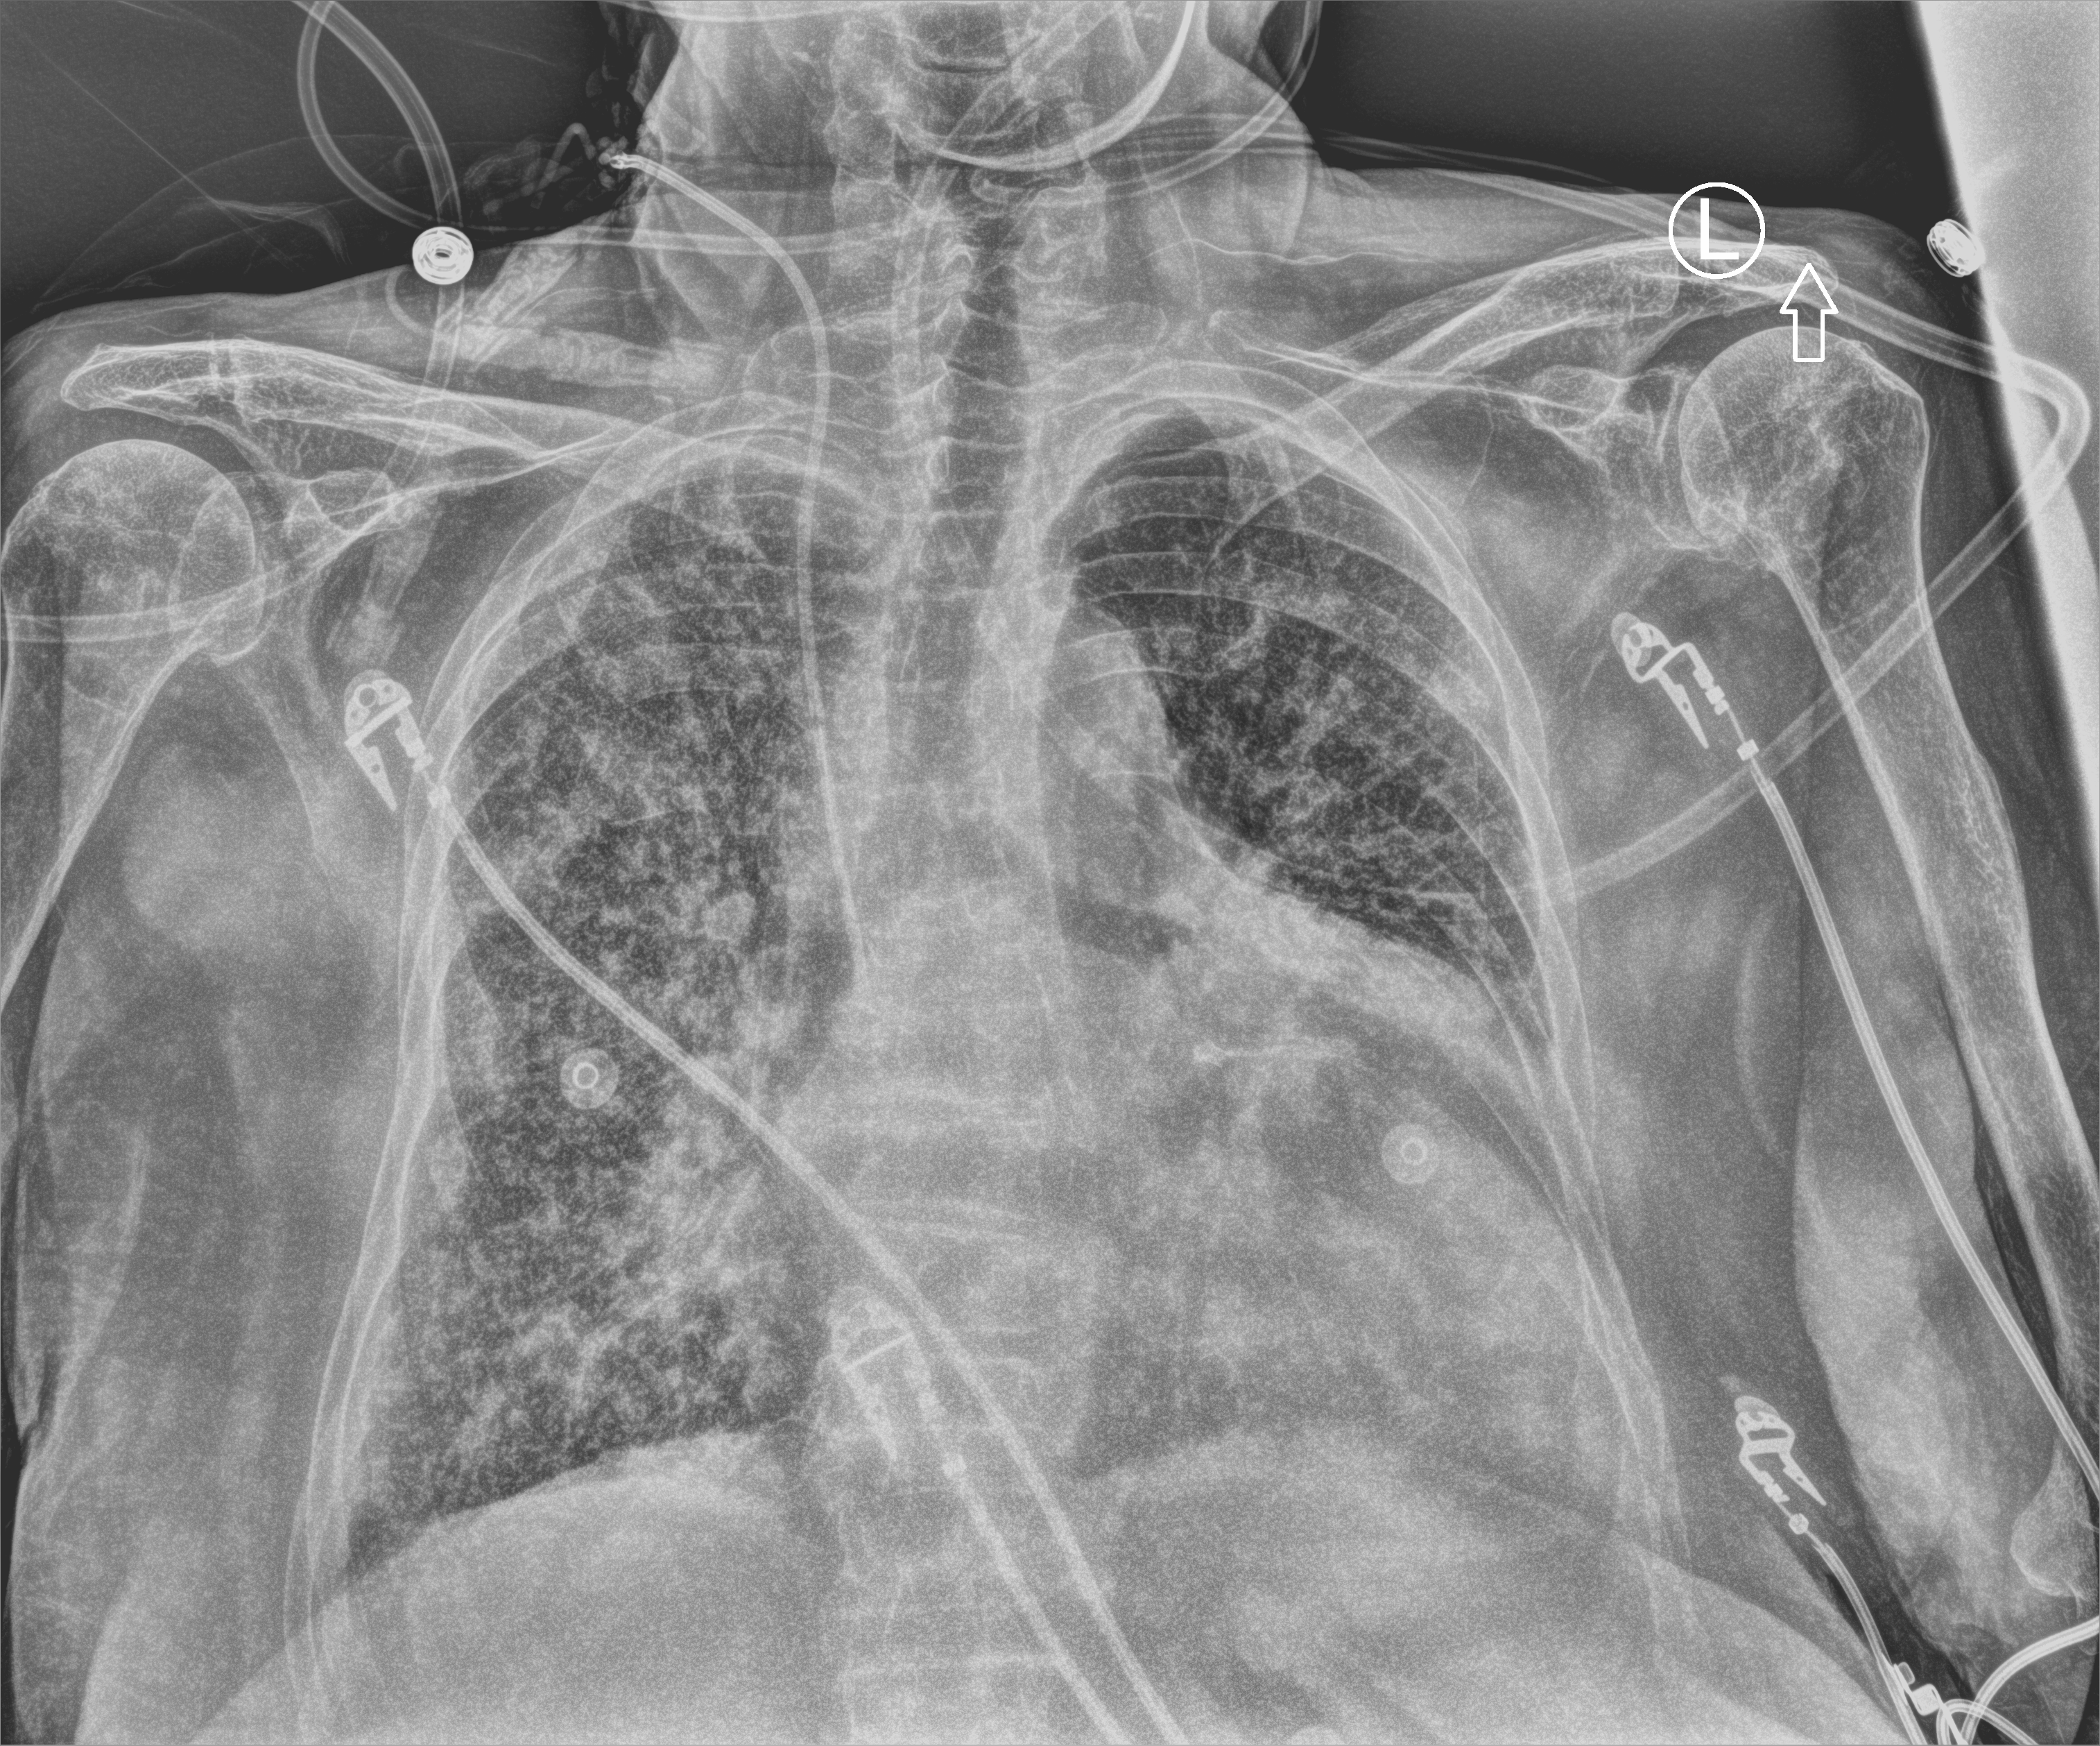
Bedside chest radiograph (computed radiography); anteroposterior (AP) projection. Female patient hospitalised with COVID-19, age 75–90 years.
From the hospital-stay record, not from the radiograph (when in the stay this image was taken is not recorded): diabetes (admission record): yes.